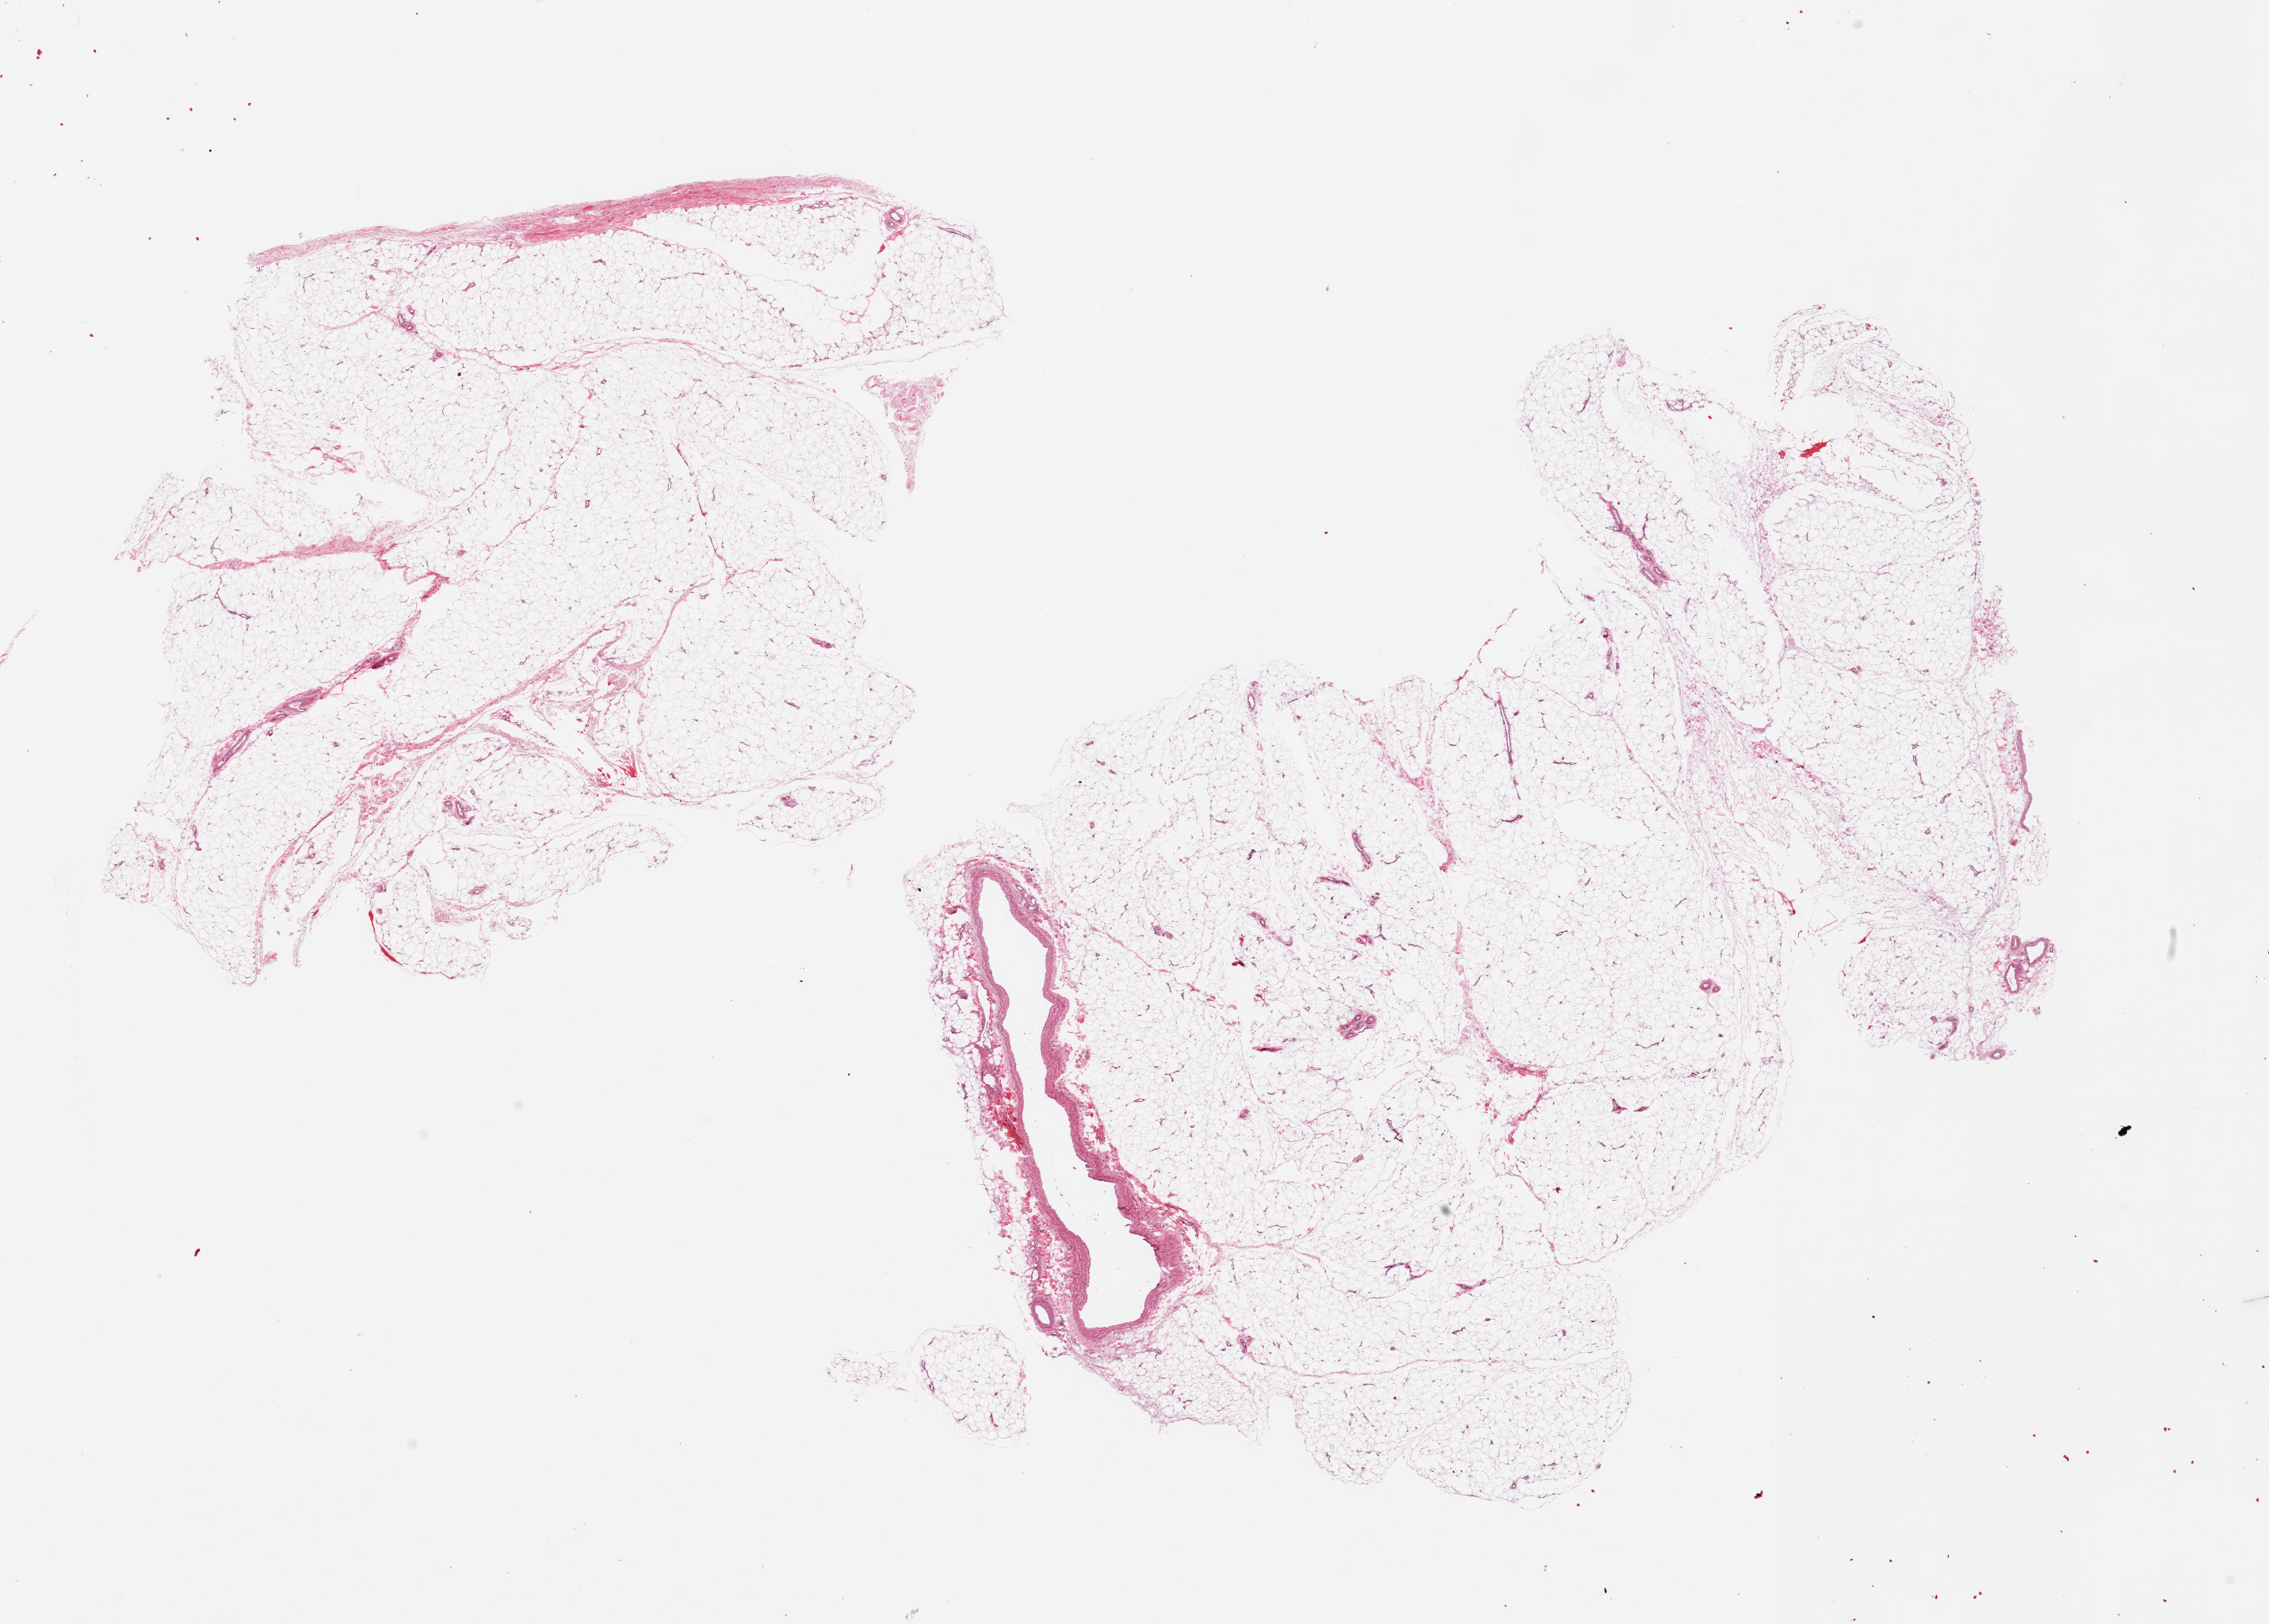
H&E whole-slide image, low-resolution overview of the scanned area, about 22.6 x 16.2 mm (from a 20x scan). PAXgene-fixed paraffin-embedded (PFPE) section. Target tissue: adipose tissue. Donor tissue sample. Donor sex: male.
Pathologist's review note for this sample: 2 pieces; mature adipose tissue with large vessel at one edge.